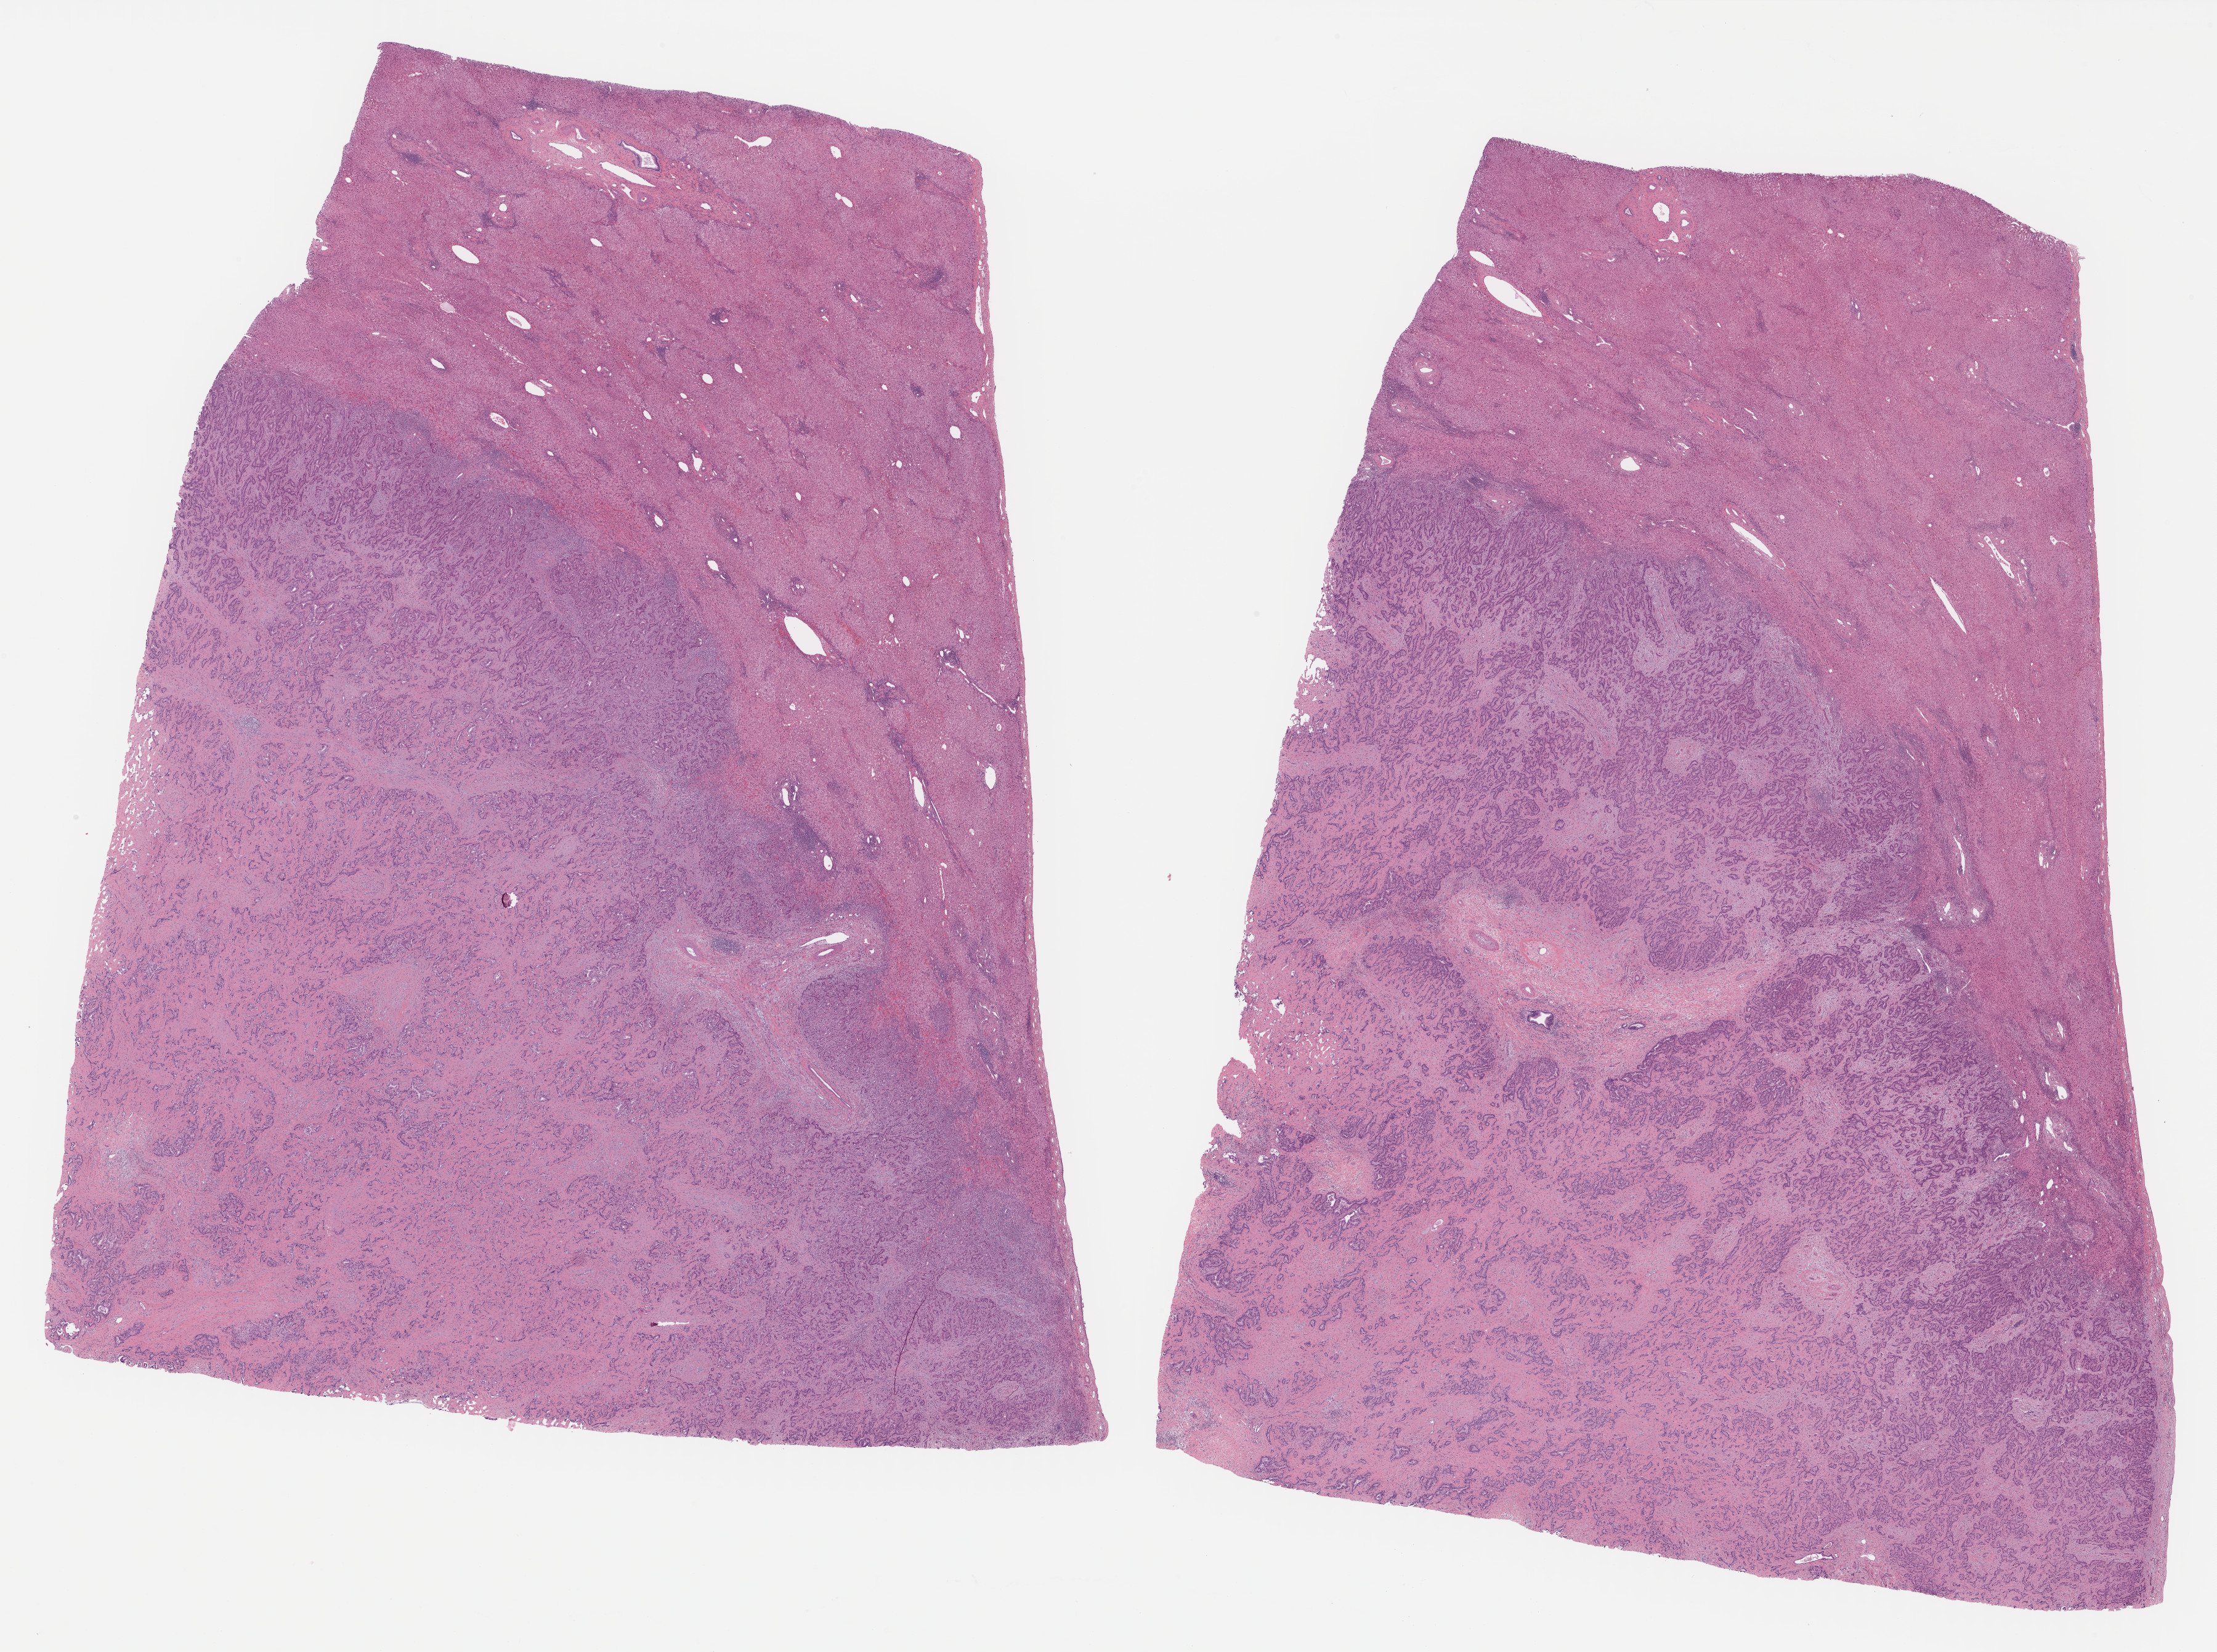
Digitized H&E tissue section (whole slide) — whole scanned area (about 29.1 x 21.7 mm) shown as a low-resolution overview; formalin-fixed paraffin-embedded (FFPE) diagnostic section; primary tumour sample from the bile duct. Male patient; age at initial diagnosis 82 years. Histologic grade: G3 (poorly differentiated).
AJCC pathologic stage: I (7th edition). Diagnosis: Cholangiocarcinoma (intrahepatic bile duct).